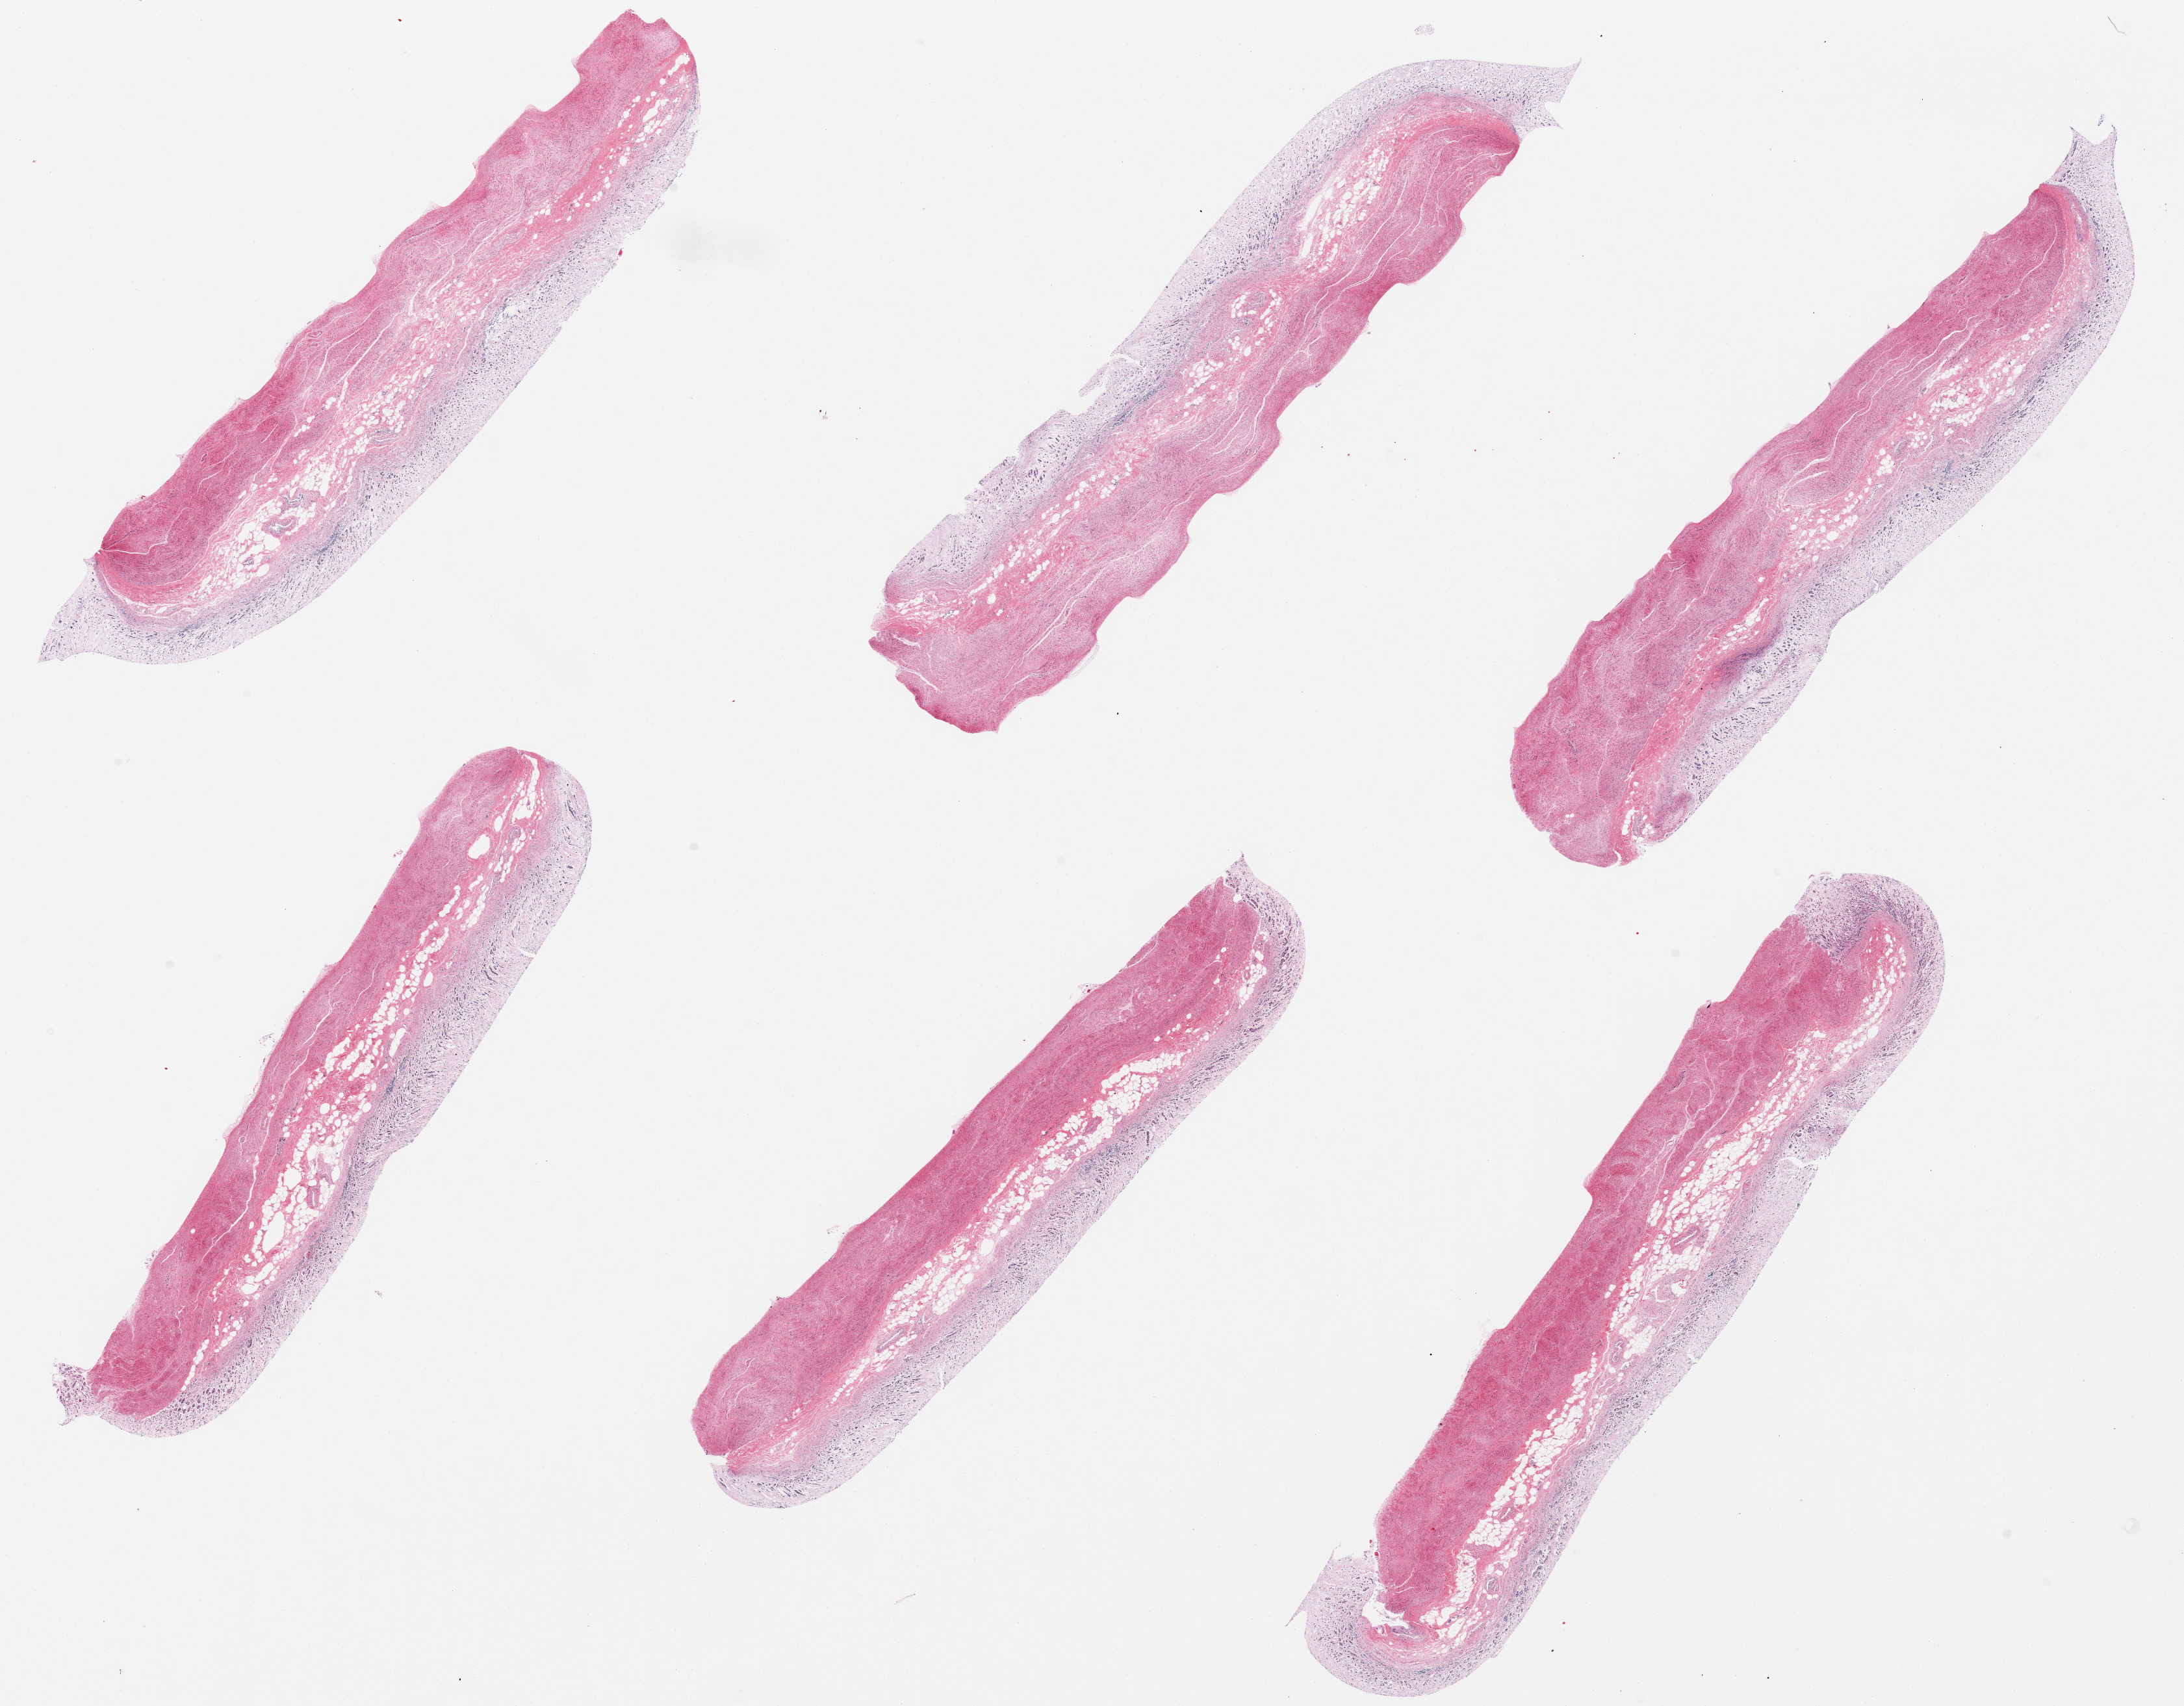
Digitized hematoxylin and eosin (H&E)-stained section, whole scanned area (about 26.6 x 20.8 mm) shown as a low-resolution overview; PAXgene-fixed, paraffin-embedded tissue; sampled site (target tissue): stomach; tissue donor sample. Male donor.
Reviewer comment on this tissue sample: 6 pieces: mucosa totally autolyzed; muscularis = 2.